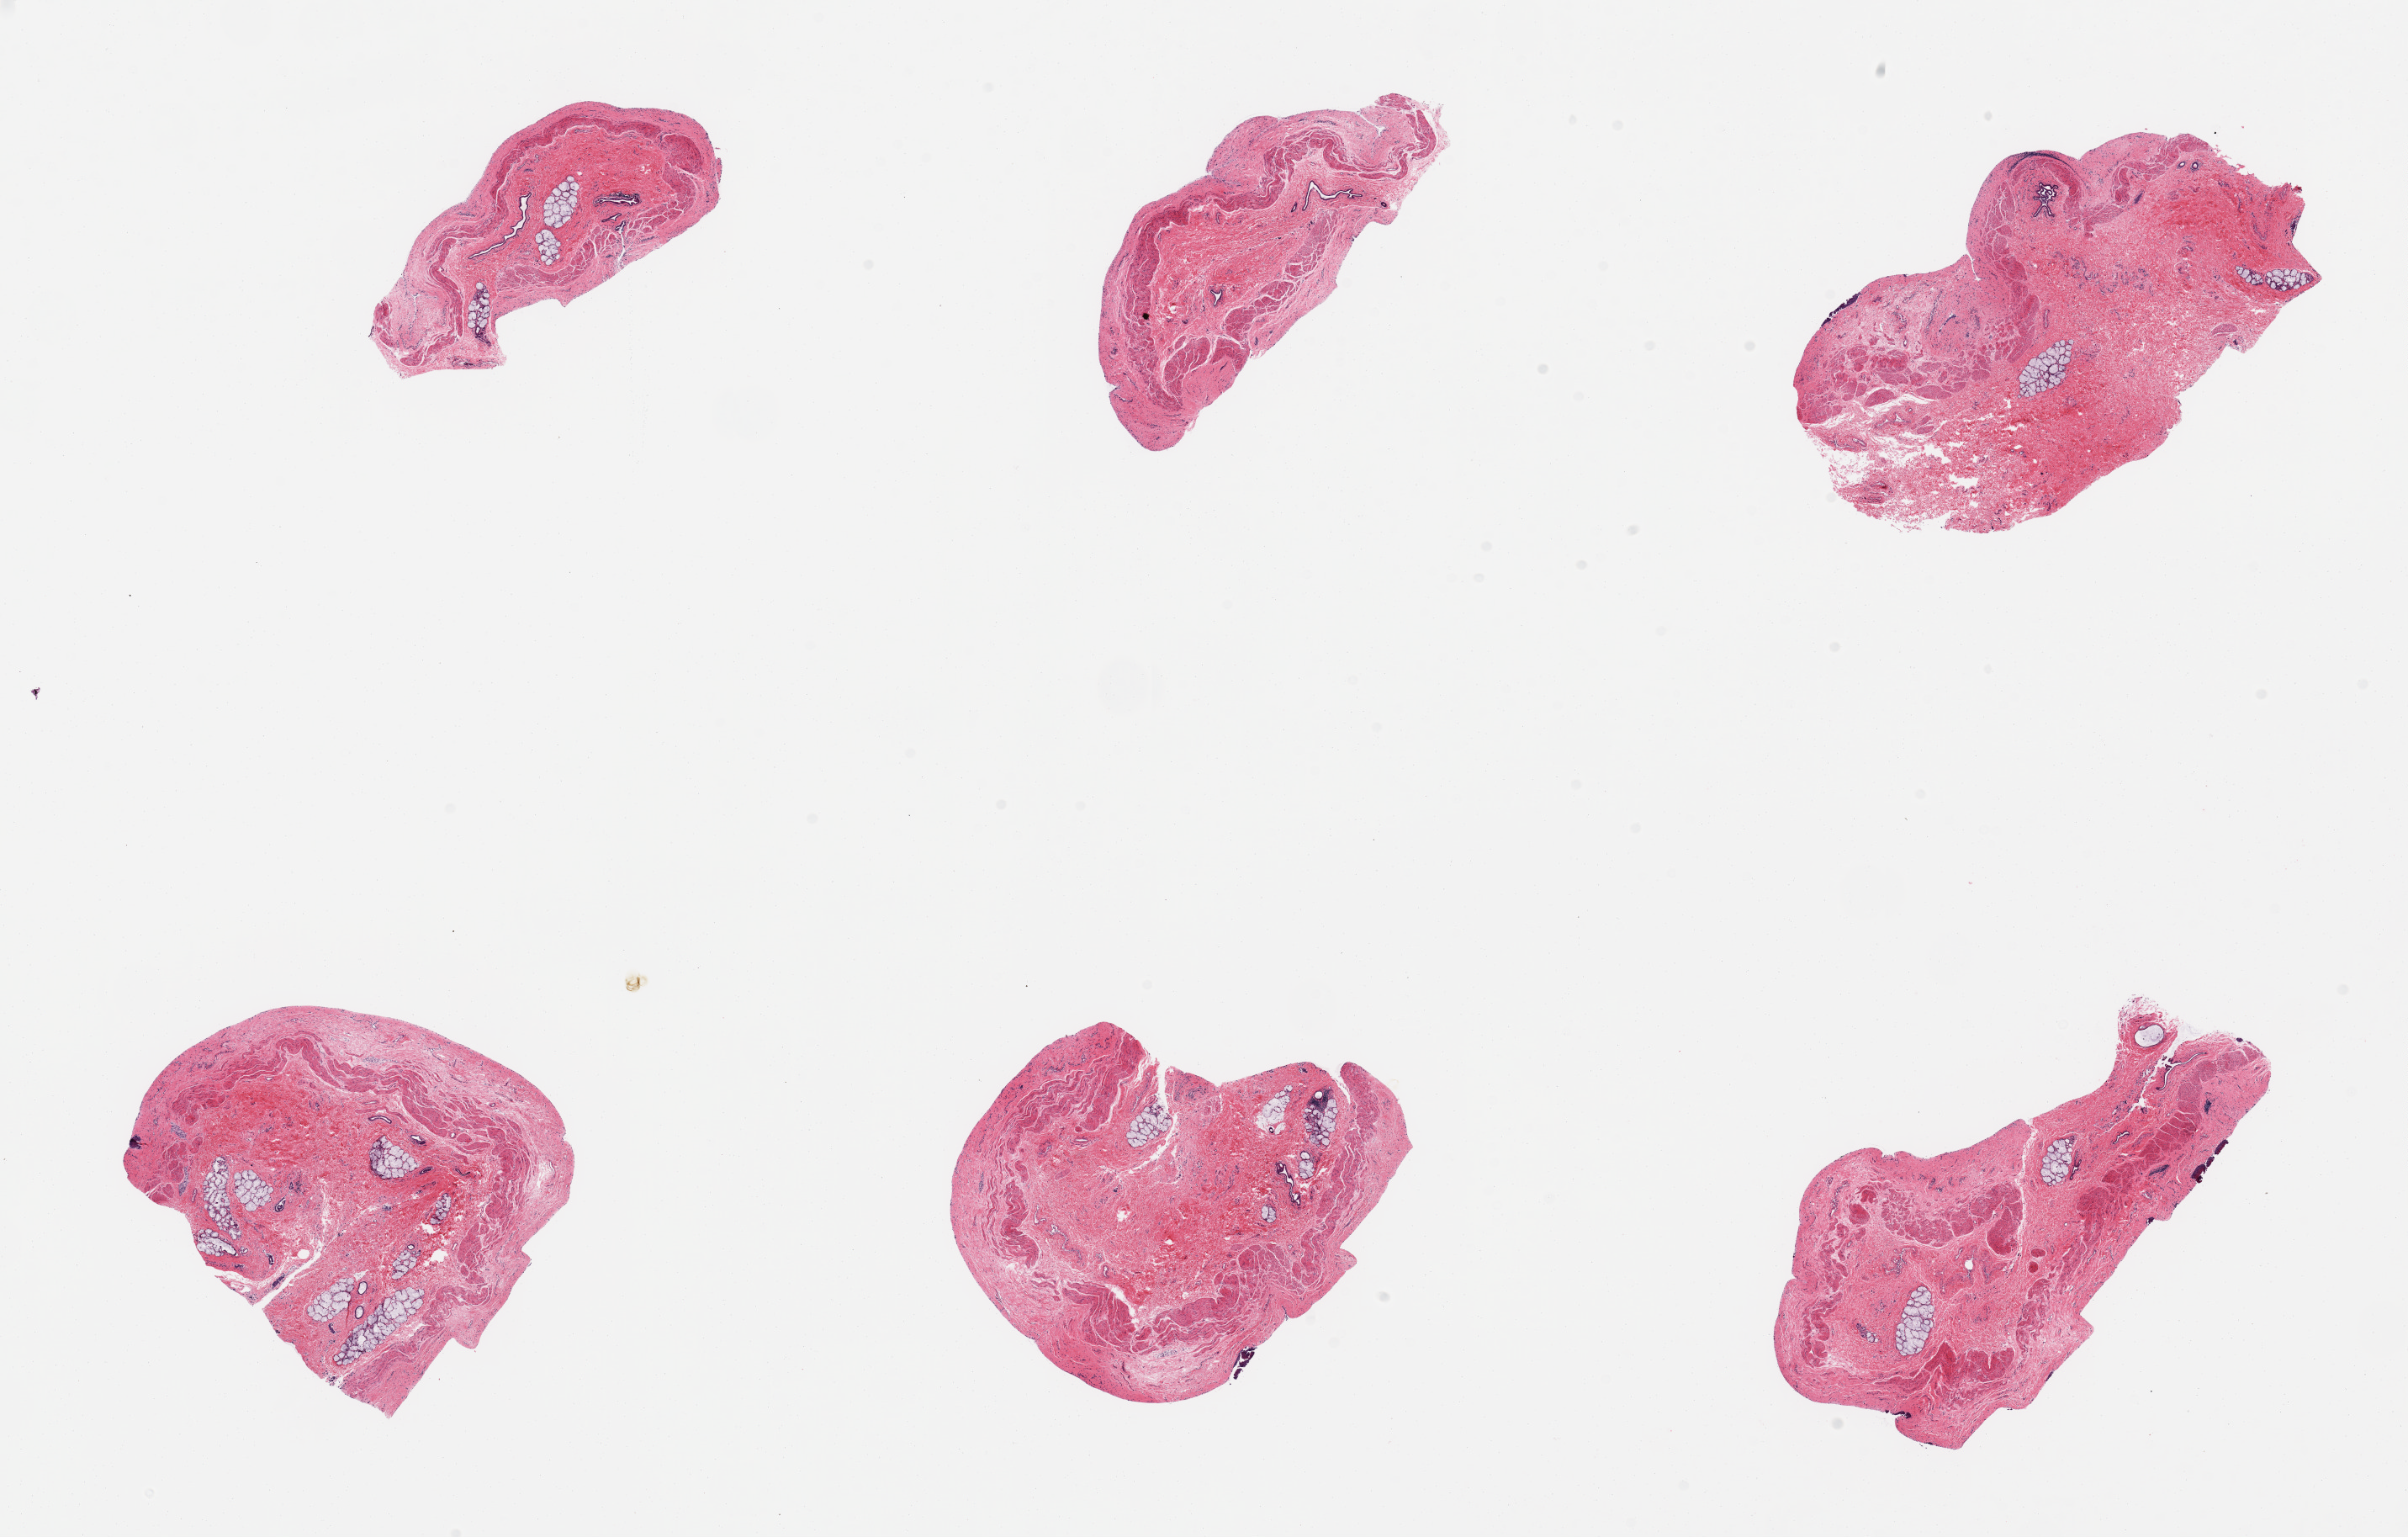
Digitized H&E-stained section — low-resolution overview of the scanned area, about 22.6 x 14.4 mm. Female donor.
Specimen: PAXgene-fixed paraffin-embedded (PFPE) section; sampled site (target tissue): esophageal mucous membrane; donor tissue sample.